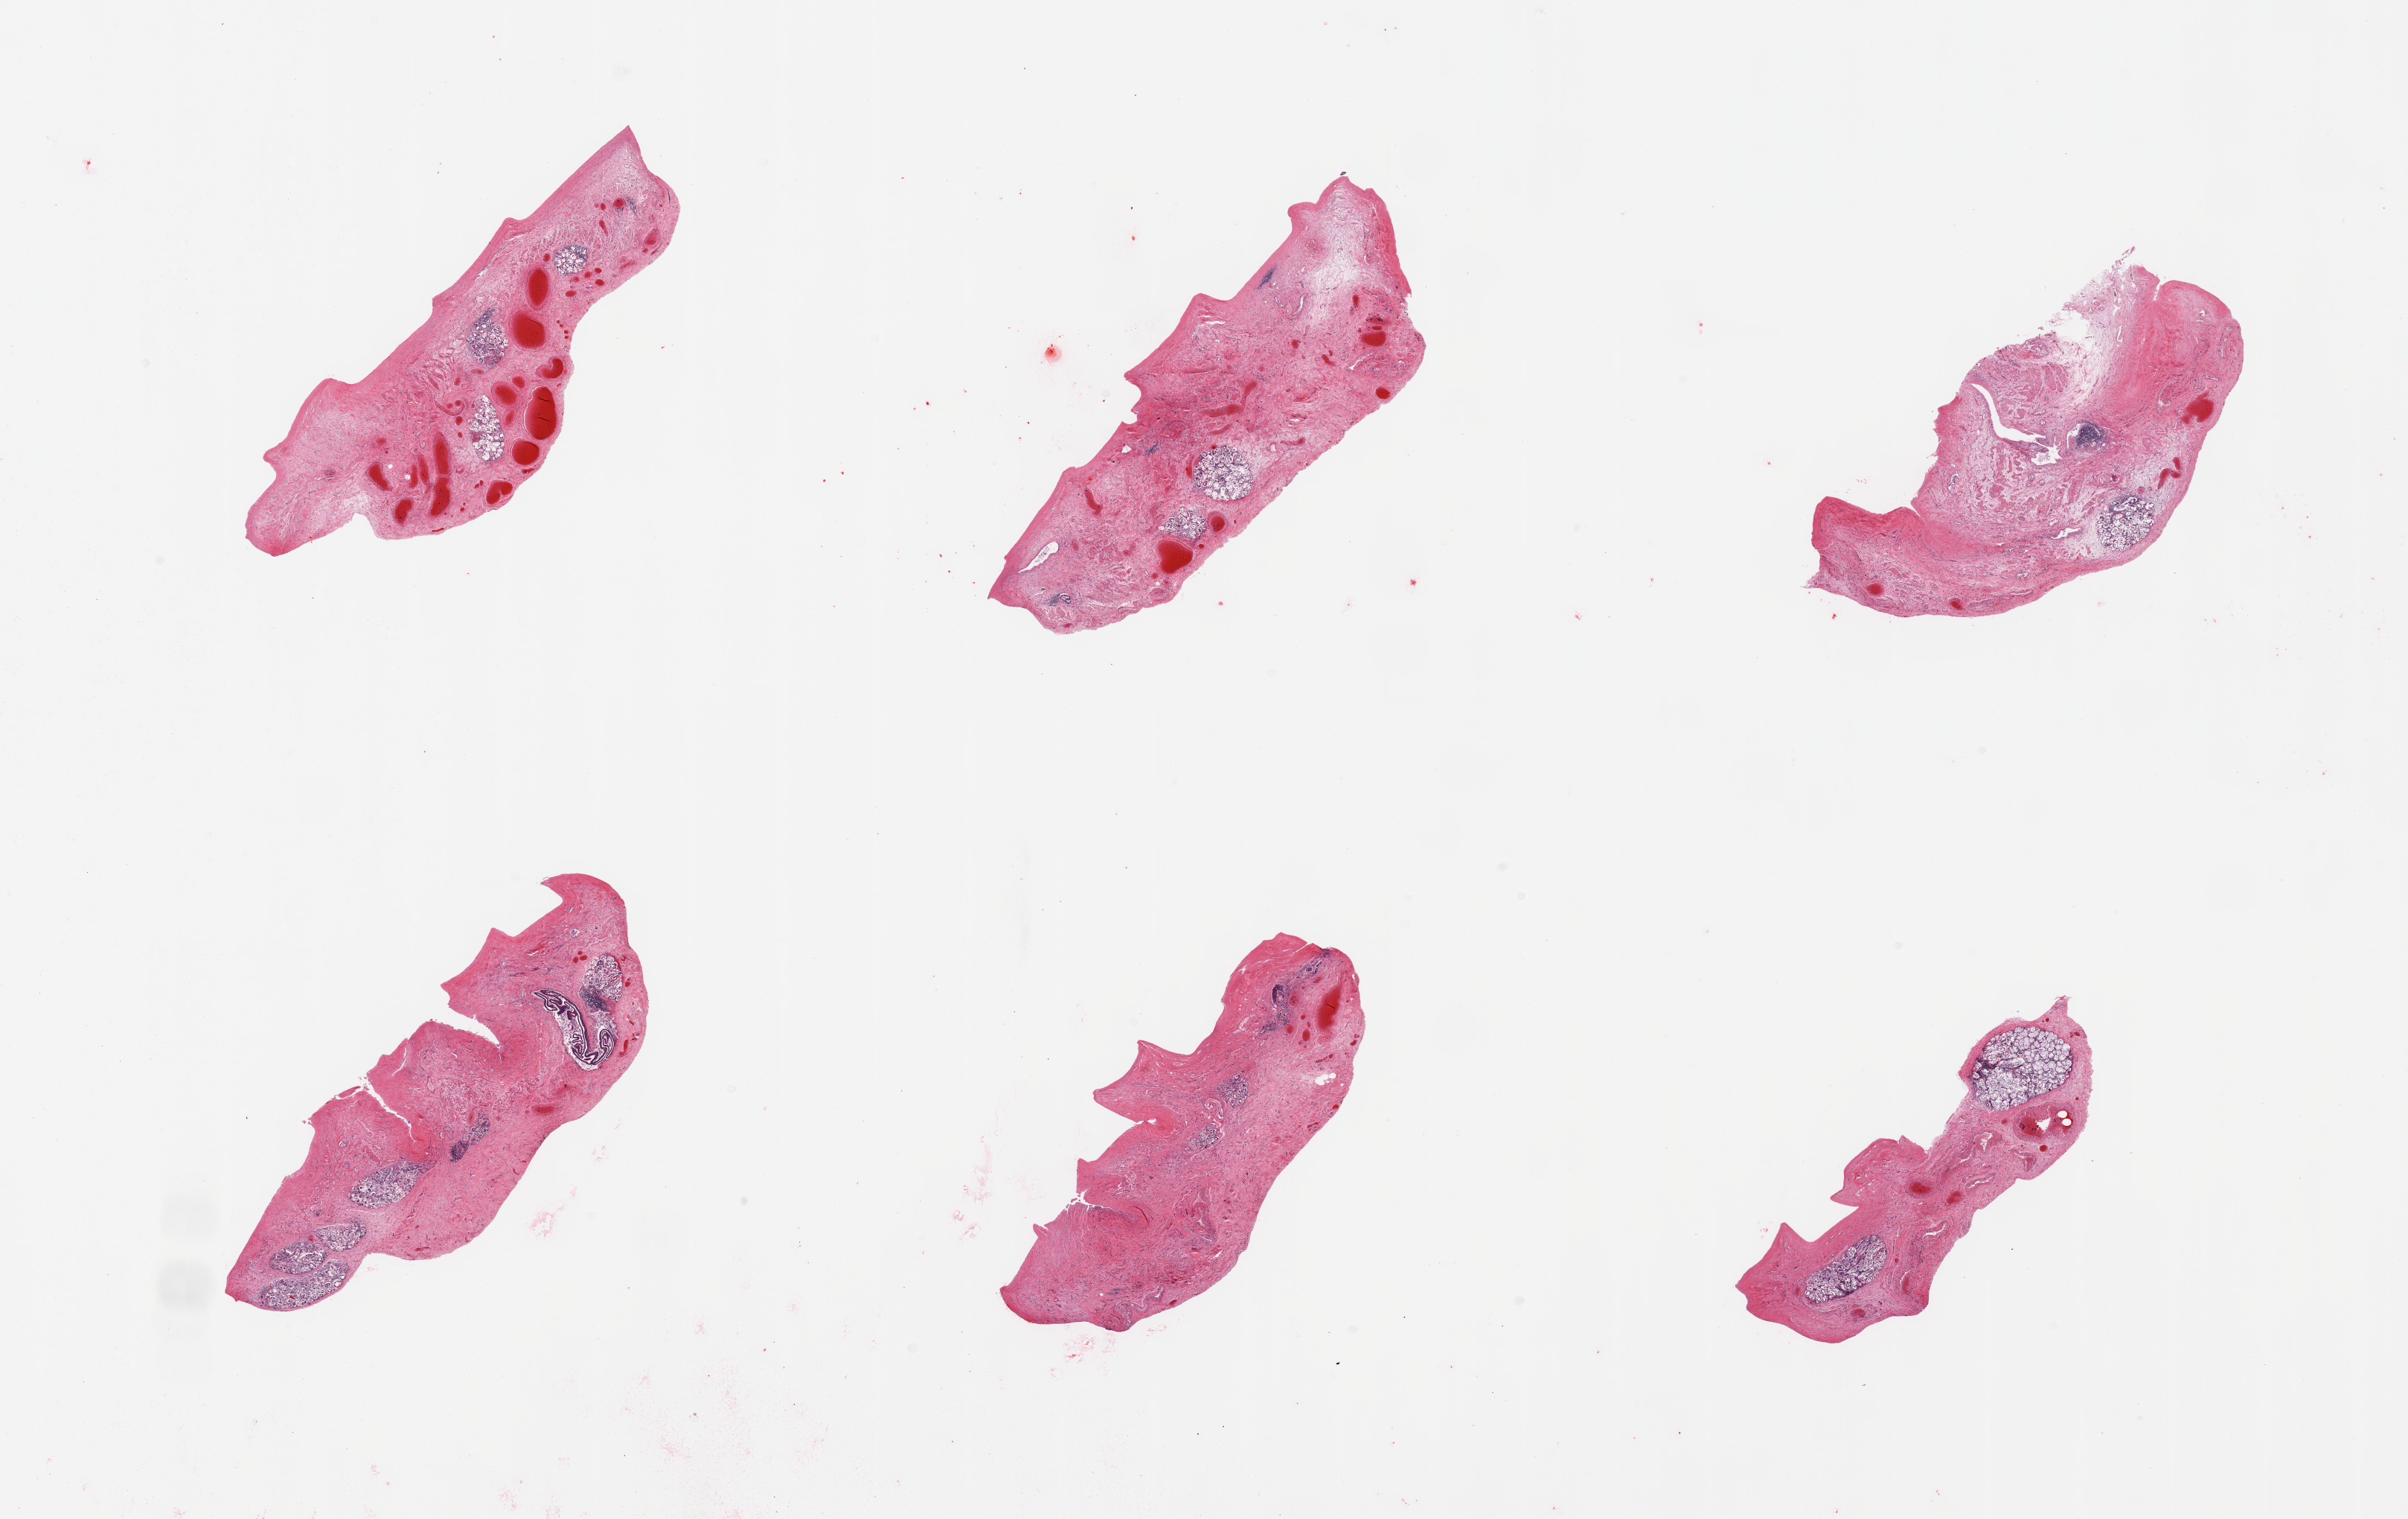
Digitized haematoxylin and eosin-stained section, brightfield — low-resolution overview of the scanned area, about 25.6 x 16.1 mm, PAXgene-fixed, paraffin-embedded tissue, sampled site (target tissue): esophageal mucous membrane, donor tissue sample. Female donor.
* review note (as recorded): 6 pieces; completely autolyzed